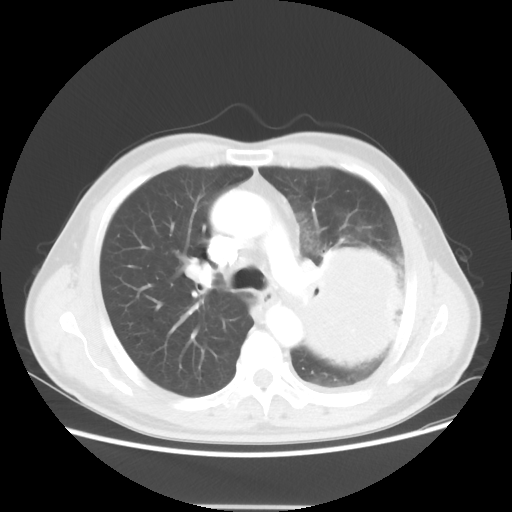
Chest CT, one axial slice; slice 35 of 53 in the series (ordered by position); lung window (W 1500 / L -600 HU); 5 mm slice thickness; 512 × 512 image matrix, field of view 391 × 391 mm. Male patient, age 60 years. From the clinical record (not read from this slice): clinical TNM (as recorded): T4 N1 M1a; histopathological grade: G3.
Annotated regions visible in this slice (rectangle marked by the reading radiologist):
- lung tumour (recorded histology: large cell carcinoma): box from (x=277, y=234) to (x=407, y=386) px